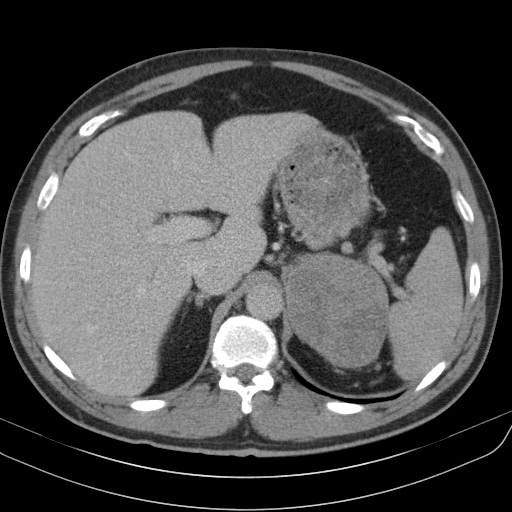
Contrast-enhanced abdominal CT, one axial slice. Position 74 of 91 along the scan axis. Reconstruction kernel B31s. 130 kVp. Intravenous contrast given. Soft-tissue window (W 400 / L 40 HU). 512 × 512 image matrix, field of view 370 × 370 mm. Male patient, age 51 years. From the clinical record (not read from this slice): diagnosis: adrenocortical carcinoma; tumour side: left adrenal; tumour size at pathology: 18 cm; Ki-67 index: 40 %; stage (as recorded): 3.
Structures marked on this image (semi-automatically segmented with operator editing):
- mass: box from (x=288, y=258) to (x=386, y=365) px